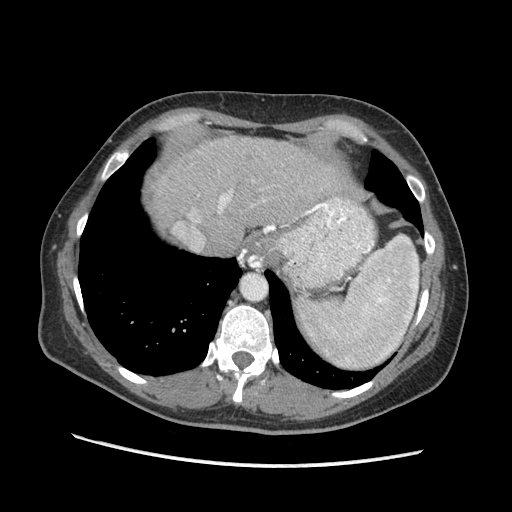
Contrast-enhanced abdominal CT (liver protocol), one axial slice; 140 kVp; soft-tissue window (W 400 / L 40 HU); 2.5 mm slice thickness; 512 × 512 image matrix, field of view 360 × 360 mm. Case-level facts recorded for this patient, not image findings: diagnosis: hepatocellular carcinoma (patient treated with transarterial chemoembolisation; whether this scan precedes or follows treatment is not stated here); TNM stage (as recorded): Stage-II; Child-Pugh class: A; tumour differentiation: no biopsy; tumour nodularity: multinodular.
Structures marked on this image (semi-automatic segmentation, software-assisted and operator-edited):
- abdominal aorta: bounding box <242,274,266,299> (left, top, right, bottom; pixels)
- liver parenchyma outside the tumour (the mass and vessels are separate outlines, so this box may not span the whole liver): <149,136,346,250>
- liver vessels: <219,192,309,232>